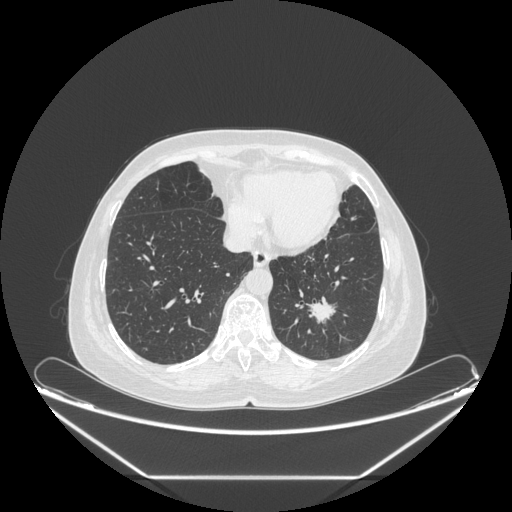
Chest CT, one axial slice. Slice 76 of 241 in the series (ordered by position). 120 kVp. Lung window (W 1500 / L -600 HU). 512 × 512 image matrix, field of view 451 × 451 mm. Female patient, age 63 years. From the clinical record (not read from this slice): clinical TNM (as recorded): T1c N0 M0; histopathological grade: G2-3.
Outlined on this slice (rectangle marked by the reading radiologist):
- lung tumour (recorded histology: adenocarcinoma): bounding box (x1, y1, x2, y2) in pixels: (303, 289, 337, 325)